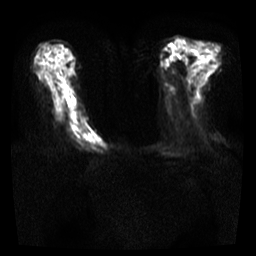
Breast MRI, one axial slice. Slice 12 of 35 in the series (ordered by position). Diffusion-weighted series; image 2 of 4 stored at this slice position (different b-values; order by instance number). 3 T. 5 mm slice thickness. 256 × 256 image matrix. Female patient.
Outlined on this slice (outlined manually by an expert reader):
- tumour on diffusion-weighted imaging: box from (x=81, y=131) to (x=103, y=149) px